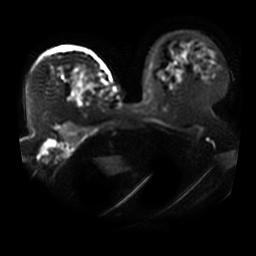
Breast MRI, one axial slice. Slice 31 of 41 in the series (ordered by position). Diffusion-weighted series; image 2 of 4 stored at this slice position (different b-values; order by instance number). 3 T. 5 mm slice thickness. 256 × 256 image matrix. Female patient.
Annotated regions visible in this slice (manually delineated by an expert):
- tumour on diffusion-weighted imaging: bounding box (x1, y1, x2, y2) in pixels: (72, 75, 83, 101)